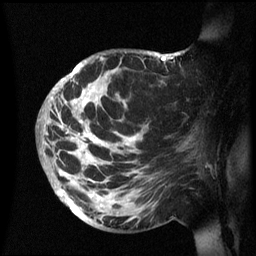
Breast MRI (dynamic contrast-enhanced), one sagittal slice; slice 38 of 60 in the series (ordered by position); dynamic contrast-enhanced series, image 2 of 3 at this slice position (ordered by acquisition); 1.5 T; TE 4.2 ms, TR 8.4 ms; 2.4 mm slice thickness; 256 × 256 image matrix, field of view 230 × 230 mm. Patient: female, 48 years.
Structures marked on this image (semi-automatic segmentation, software-assisted and operator-edited):
- analysis volume of interest (the breast-tissue region the enhancement analysis was run in; not a lesion): bounding box <42,51,202,236> (left, top, right, bottom; pixels)
- tumour enhancement mask (voxels above the 70 % enhancement threshold inside the analysis volume of interest): <44,53,180,211>